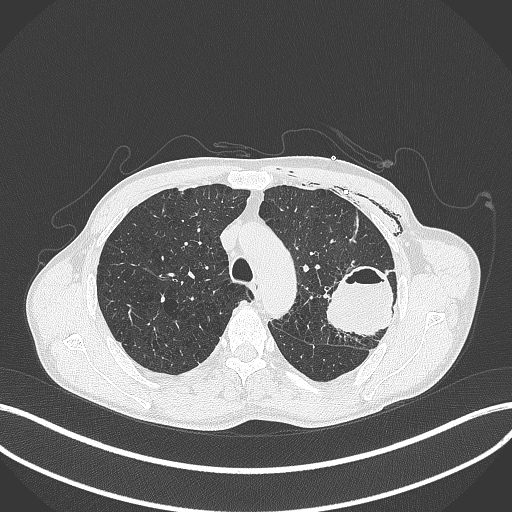
Chest CT, one axial slice. Position 298 of 457 along the scan axis. Reconstruction kernel B70f. Lung window (W 1500 / L -600 HU). 1 mm slice thickness. 512 × 512 image matrix, field of view 400 × 400 mm. Patient: male, 58 years. From the clinical record (not read from this slice): clinical TNM (as recorded): T3 N0 M0.
Structures marked on this image (bounding box drawn by a radiologist):
- lung tumour (recorded histology: adenocarcinoma): bounding box <325,261,398,339> (left, top, right, bottom; pixels)